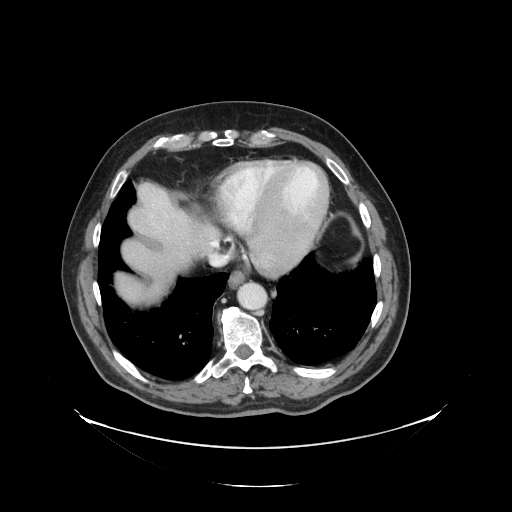
Contrast-enhanced abdominal CT, one axial slice. Slice 120 of 138 in the series (ordered by position). 120 kVp. Intravenous contrast given. Soft-tissue window (W 400 / L 40 HU). 2.5 mm slice thickness. 512 × 512 image matrix, field of view 497 × 497 mm. Male patient, age 77 years. From the clinical record (not read from this slice): diagnosis: colorectal cancer liver metastases, imaged before liver resection; multiple liver metastases: no; largest metastasis: 1.5 cm; chemotherapy before resection: no.
Structures marked on this image (outlined manually by an expert reader):
- hepatic veins: box from (x=211, y=241) to (x=217, y=246) px
- liver: (x=116, y=185)–(x=218, y=303)
- planned liver remnant (the part of the liver to remain after resection): (x=116, y=185)–(x=217, y=288)